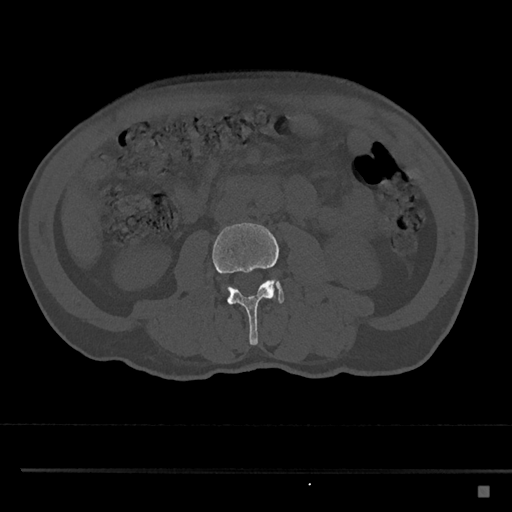
CT including the spine, one axial slice. Slice 687 of 797 in the series (ordered by position). Reconstruction kernel Br40s/3. 120 kVp. Bone window (W 1800 / L 400 HU). 512 × 512 image matrix. Patient: male, 59 years. From the clinical record (not read from this slice): primary cancer: prostate.
Annotated regions visible in this slice (semi-automatic segmentation, software-assisted and operator-edited):
- L3 vertebra: bounding box <212,222,280,345> (left, top, right, bottom; pixels)
- L4 vertebra: <224,279,284,303>